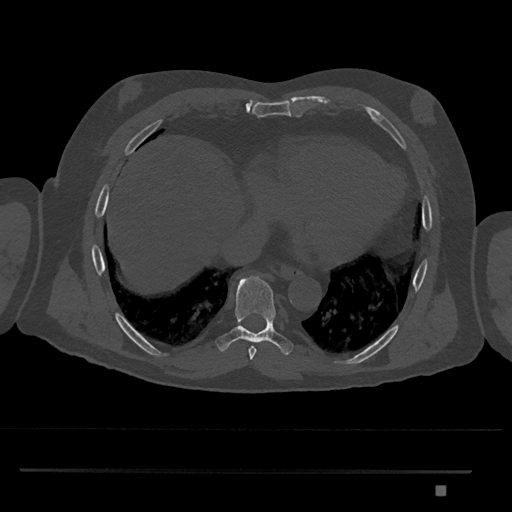
CT including the spine, one axial slice; slice 1116 of 1134 in the series (ordered by position); reconstruction kernel Br40s/3; 120 kVp; bone window (W 1800 / L 400 HU); 0.5 mm slice thickness; 512 × 512 image matrix, field of view 429 × 429 mm. Male patient, age 65 years. Case-level facts recorded for this patient, not image findings: primary cancer: prostate.
Annotated regions visible in this slice (semi-automatic segmentation, software-assisted and operator-edited):
- T8 vertebra: box from (x=215, y=275) to (x=294, y=355) px